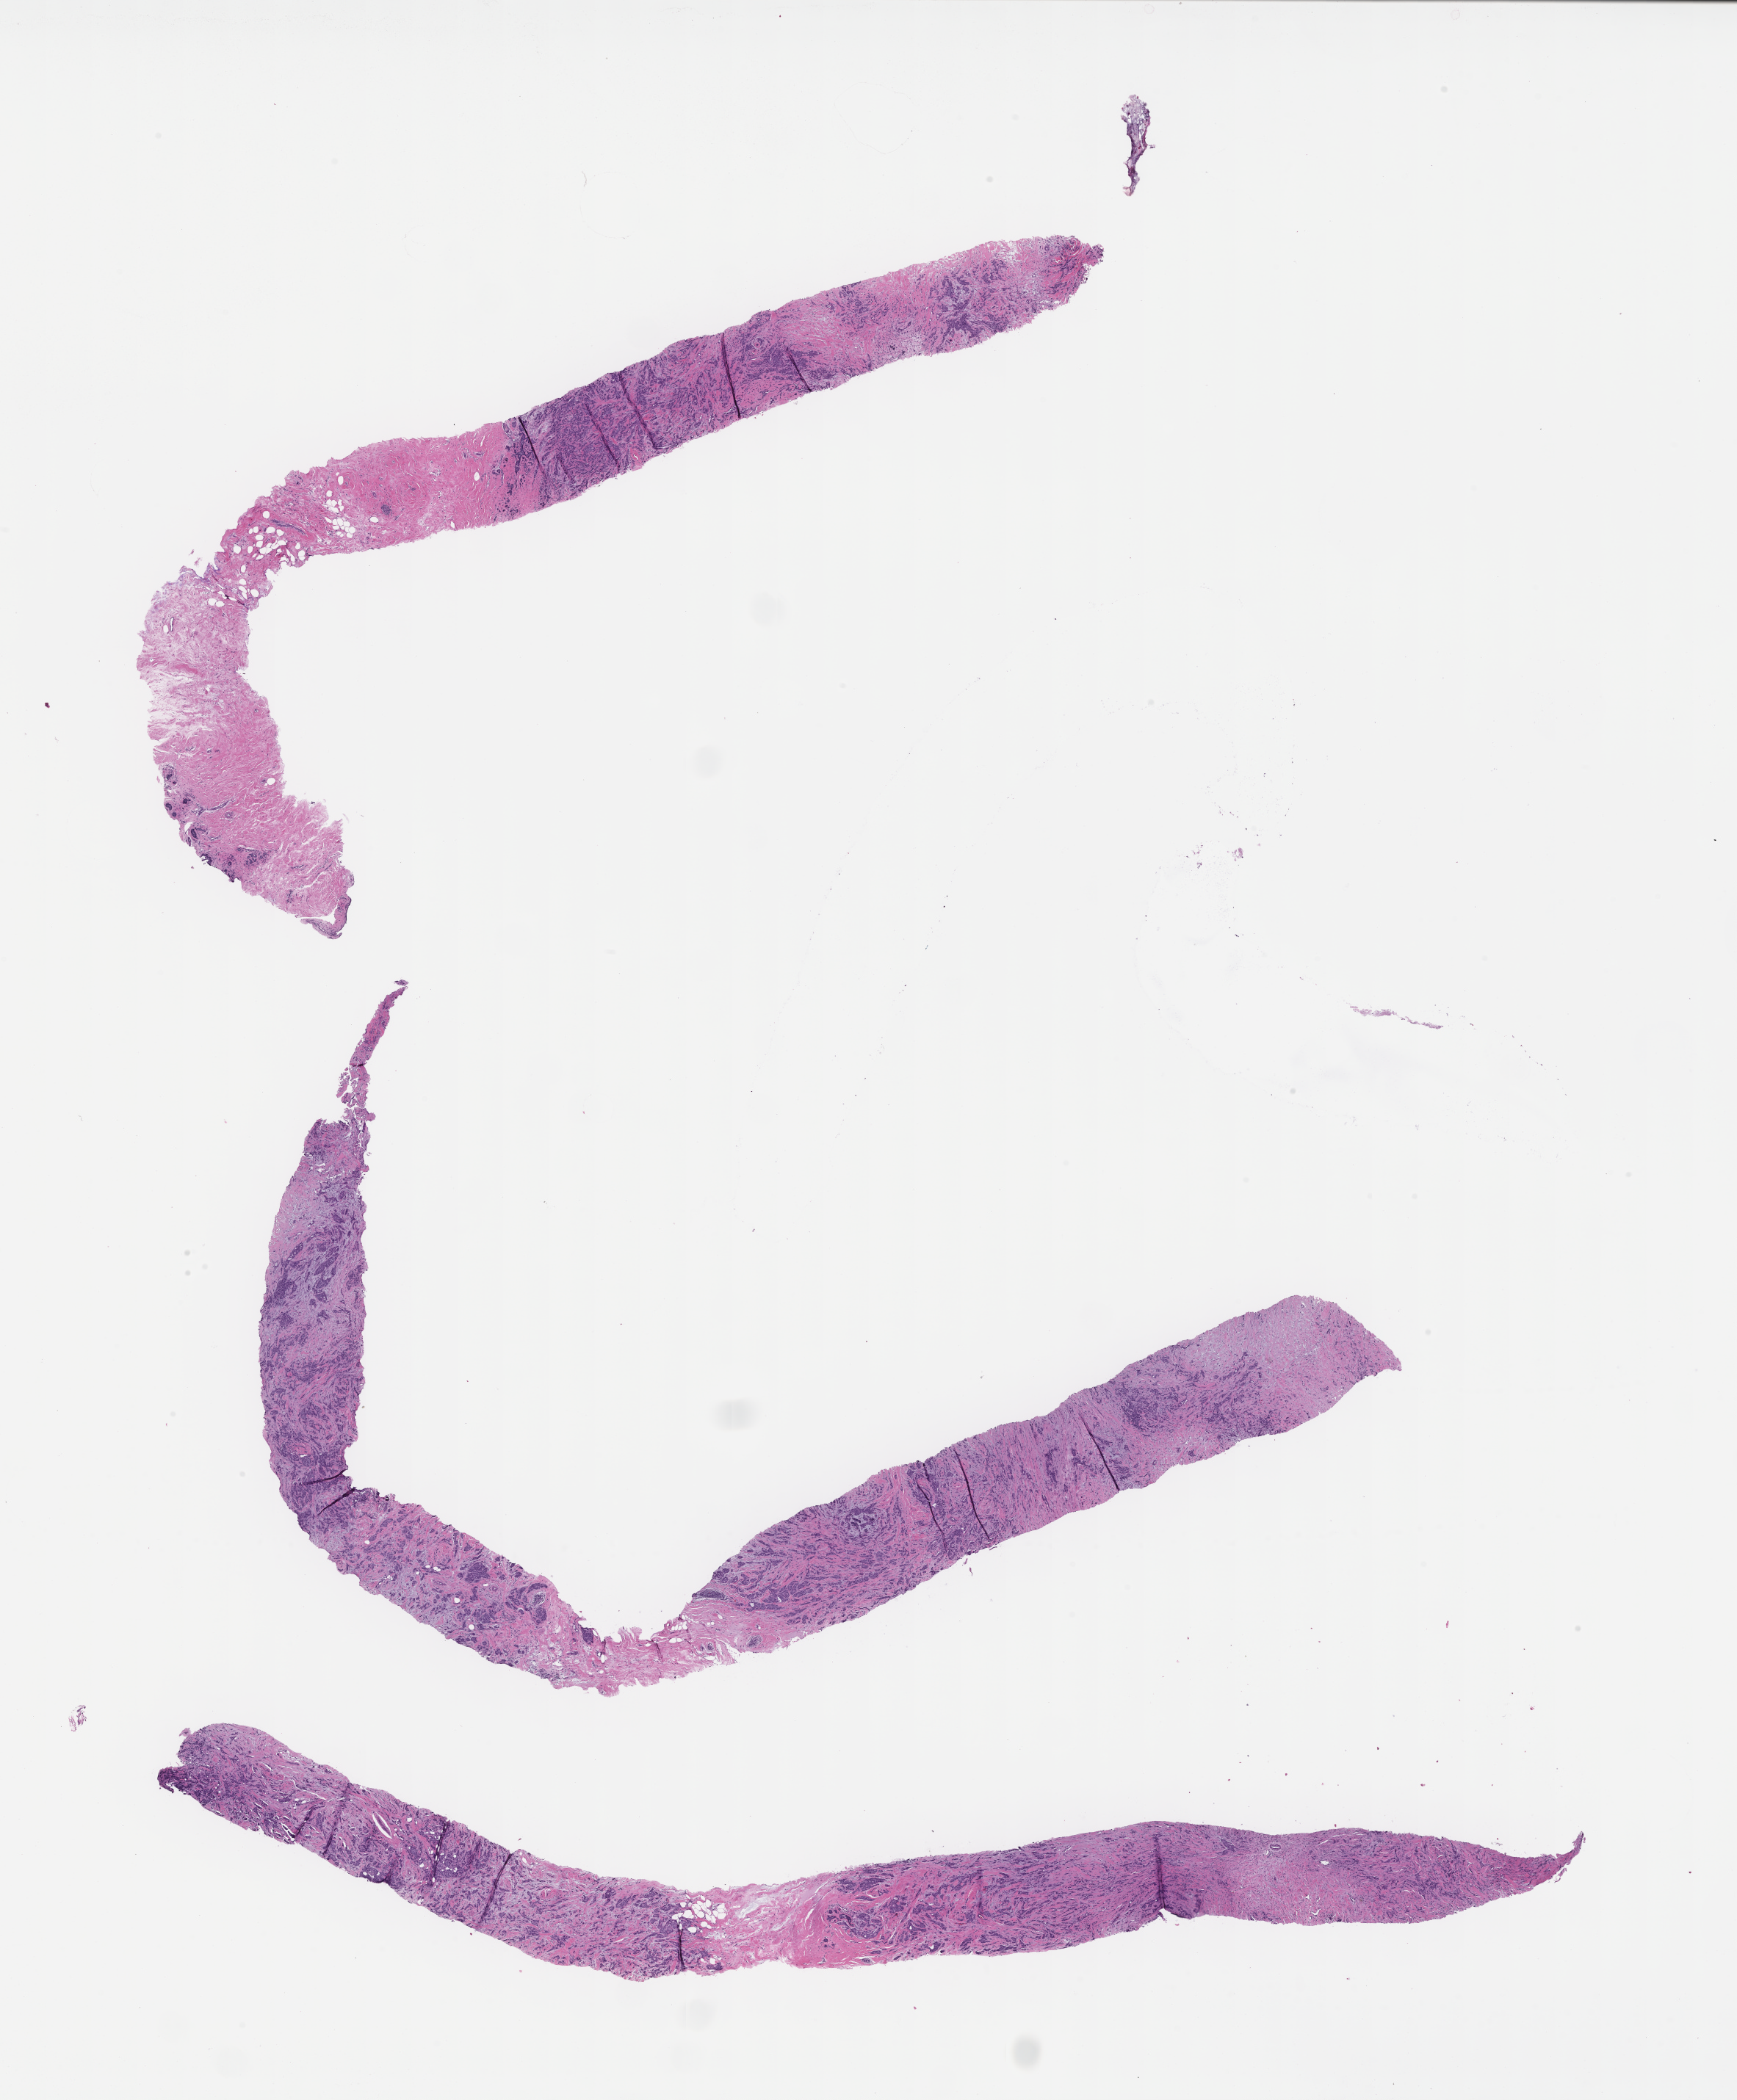
Whole-slide image, haematoxylin and eosin stain — shown as a low-resolution overview of the whole scanned area (about 19.1 x 23.1 mm); formalin-fixed, paraffin-embedded (FFPE) tissue; archival tissue. Female patient.
This section: metastasis (sampled organ not recorded). Patient diagnosis (primary): Invasive Breast Carcinoma.